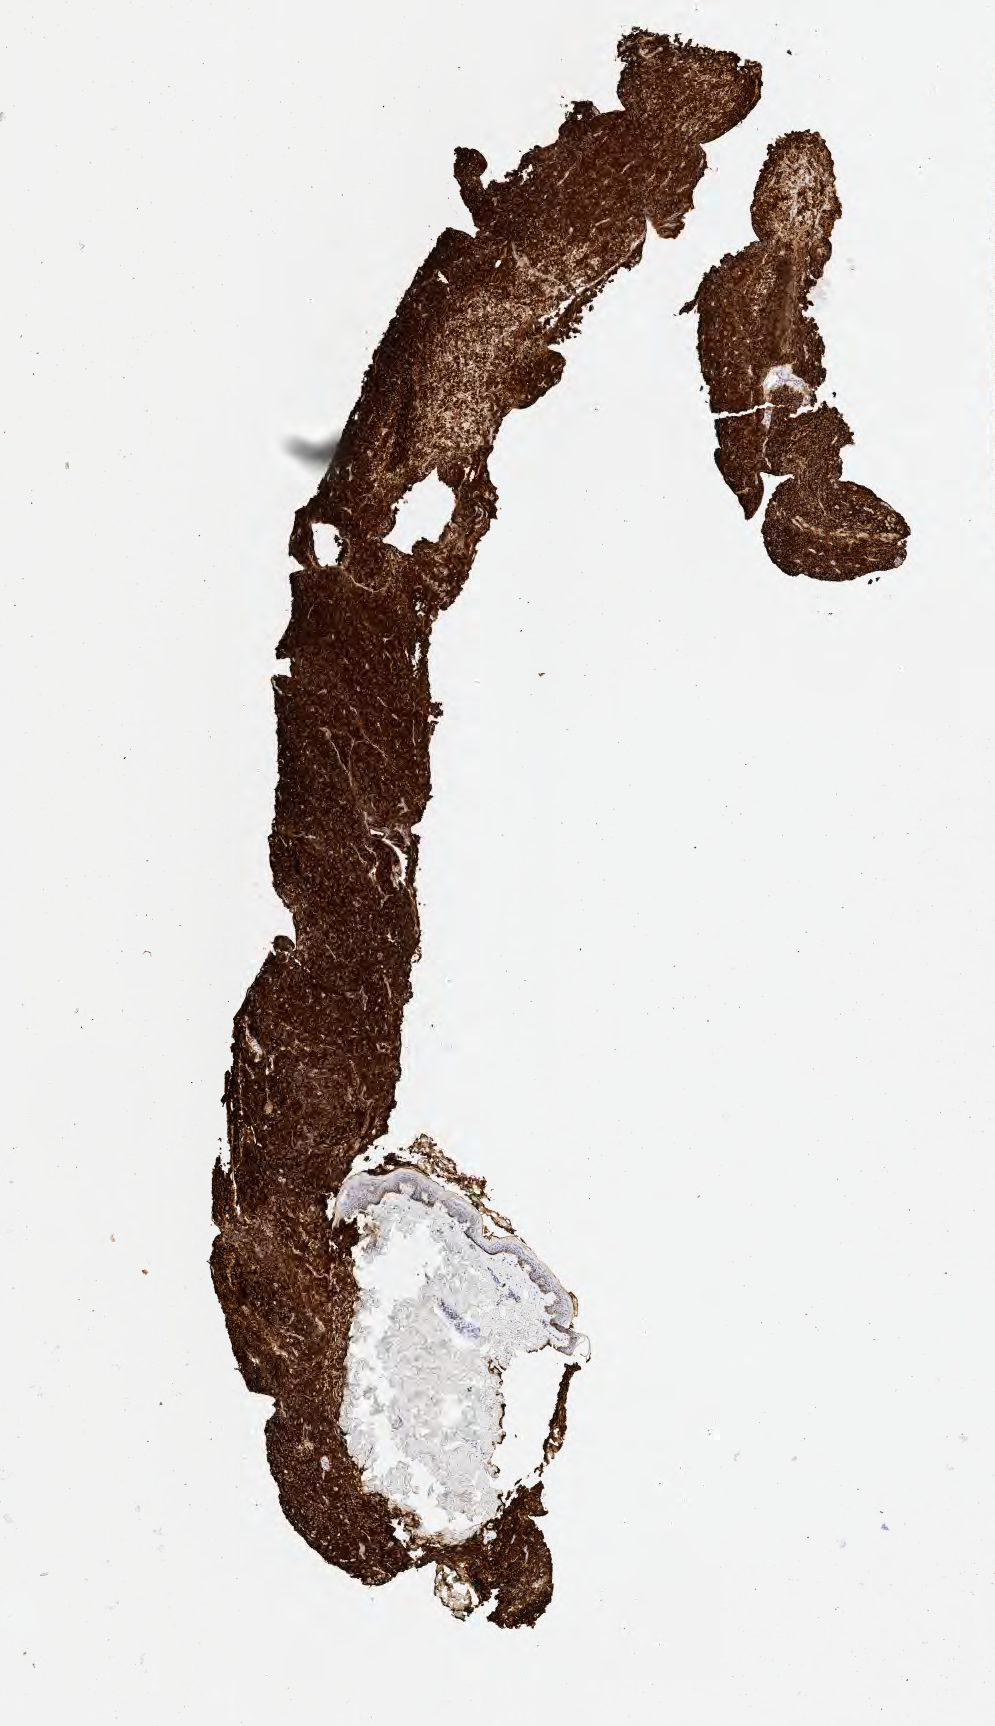
IHC for CD20, whole-slide image — shown as a low-resolution overview of the whole scanned area (about 4.0 x 7.0 mm); specimen: tumor tissue. Patient female; 43 years old.
Histologic diagnosis: Diffuse large B-cell lymphoma, NOS.